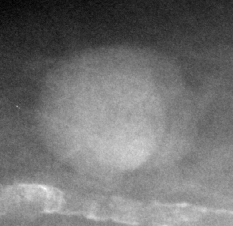
Region of interest cut from a scanned film mammogram (one marked finding), right breast, CC view, BI-RADS breast density category 1 (scale 1–4).
Mass, shape round, margins circumscribed; BI-RADS assessment category 3; pathology (as recorded): benign.